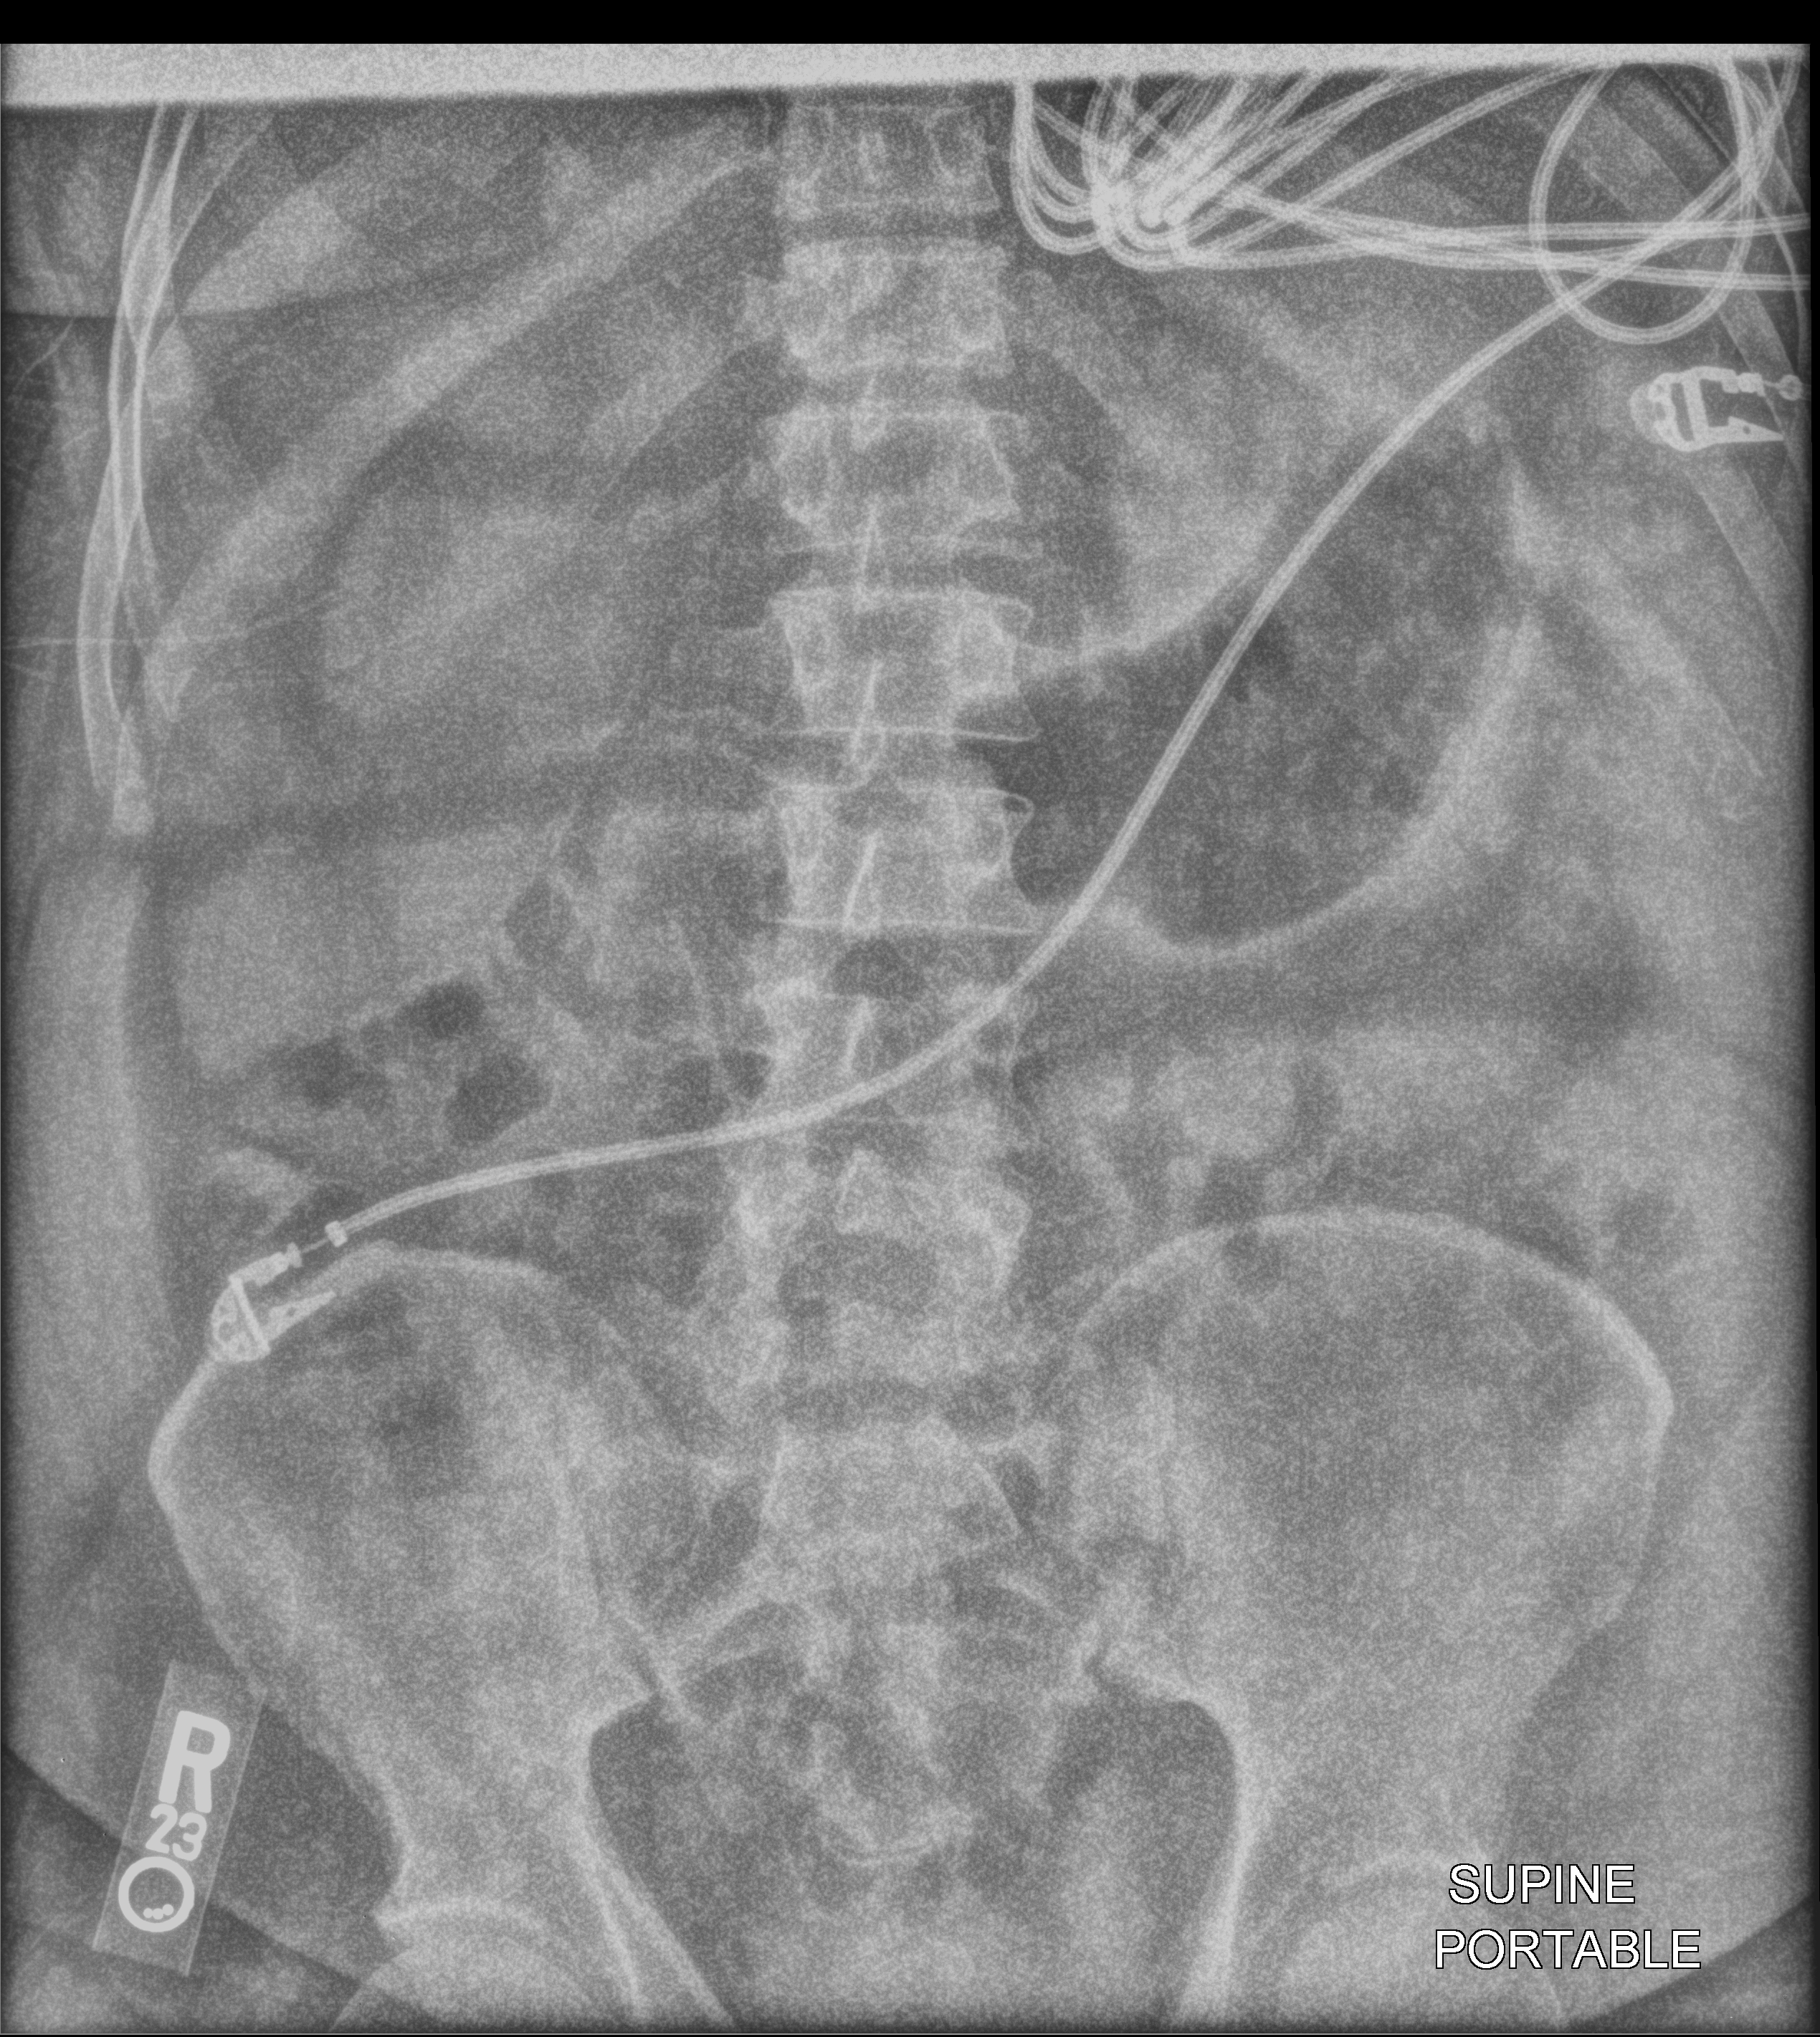
Bedside abdomen radiograph (computed radiography), anteroposterior (AP) projection. Patient hospitalised with COVID-19; male, aged 18–59 years.
Hospital-stay facts (about this admission, not read from this image; timing relative to this image not recorded): mechanically ventilated during this hospital stay: yes; admitted to intensive care during this hospital stay: yes.